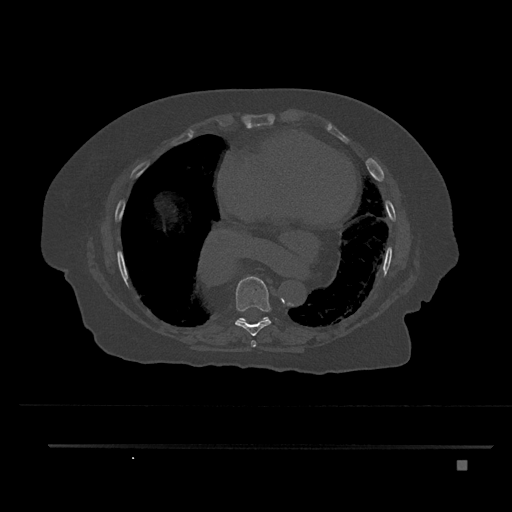
CT including the spine, one axial slice; position 435 of 797 along the scan axis; reconstruction kernel Br40s/3; 120 kVp; bone window (W 1800 / L 400 HU); 512 × 512 image matrix. Female patient, age 76 years. From the clinical record (not read from this slice): primary cancer: lung; vertebrae with lytic lesions (as recorded): T11, L3.
Outlined on this slice (semi-automatic segmentation, software-assisted and operator-edited):
- T7 vertebra: box from (x=251, y=340) to (x=256, y=347) px
- T8 vertebra: (x=235, y=276)–(x=271, y=336)
- T9 vertebra: (x=238, y=317)–(x=267, y=322)